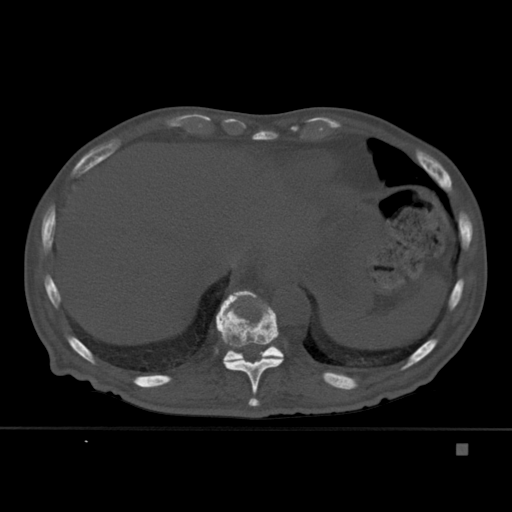
CT including the spine, one axial slice. Slice 228 of 451 in the series (ordered by position). Bone window (W 1800 / L 400 HU). 1.5 mm slice thickness. 512 × 512 image matrix, field of view 378 × 378 mm. Patient: male, 75 years. Case-level facts recorded for this patient, not image findings: primary cancer: prostate.
Structures marked on this image (semi-automatically segmented with operator editing):
- T10 vertebra: bounding box (x1, y1, x2, y2) in pixels: (216, 290, 284, 407)
- T11 vertebra: (216, 296, 284, 363)
- T9 vertebra: (249, 398, 259, 401)